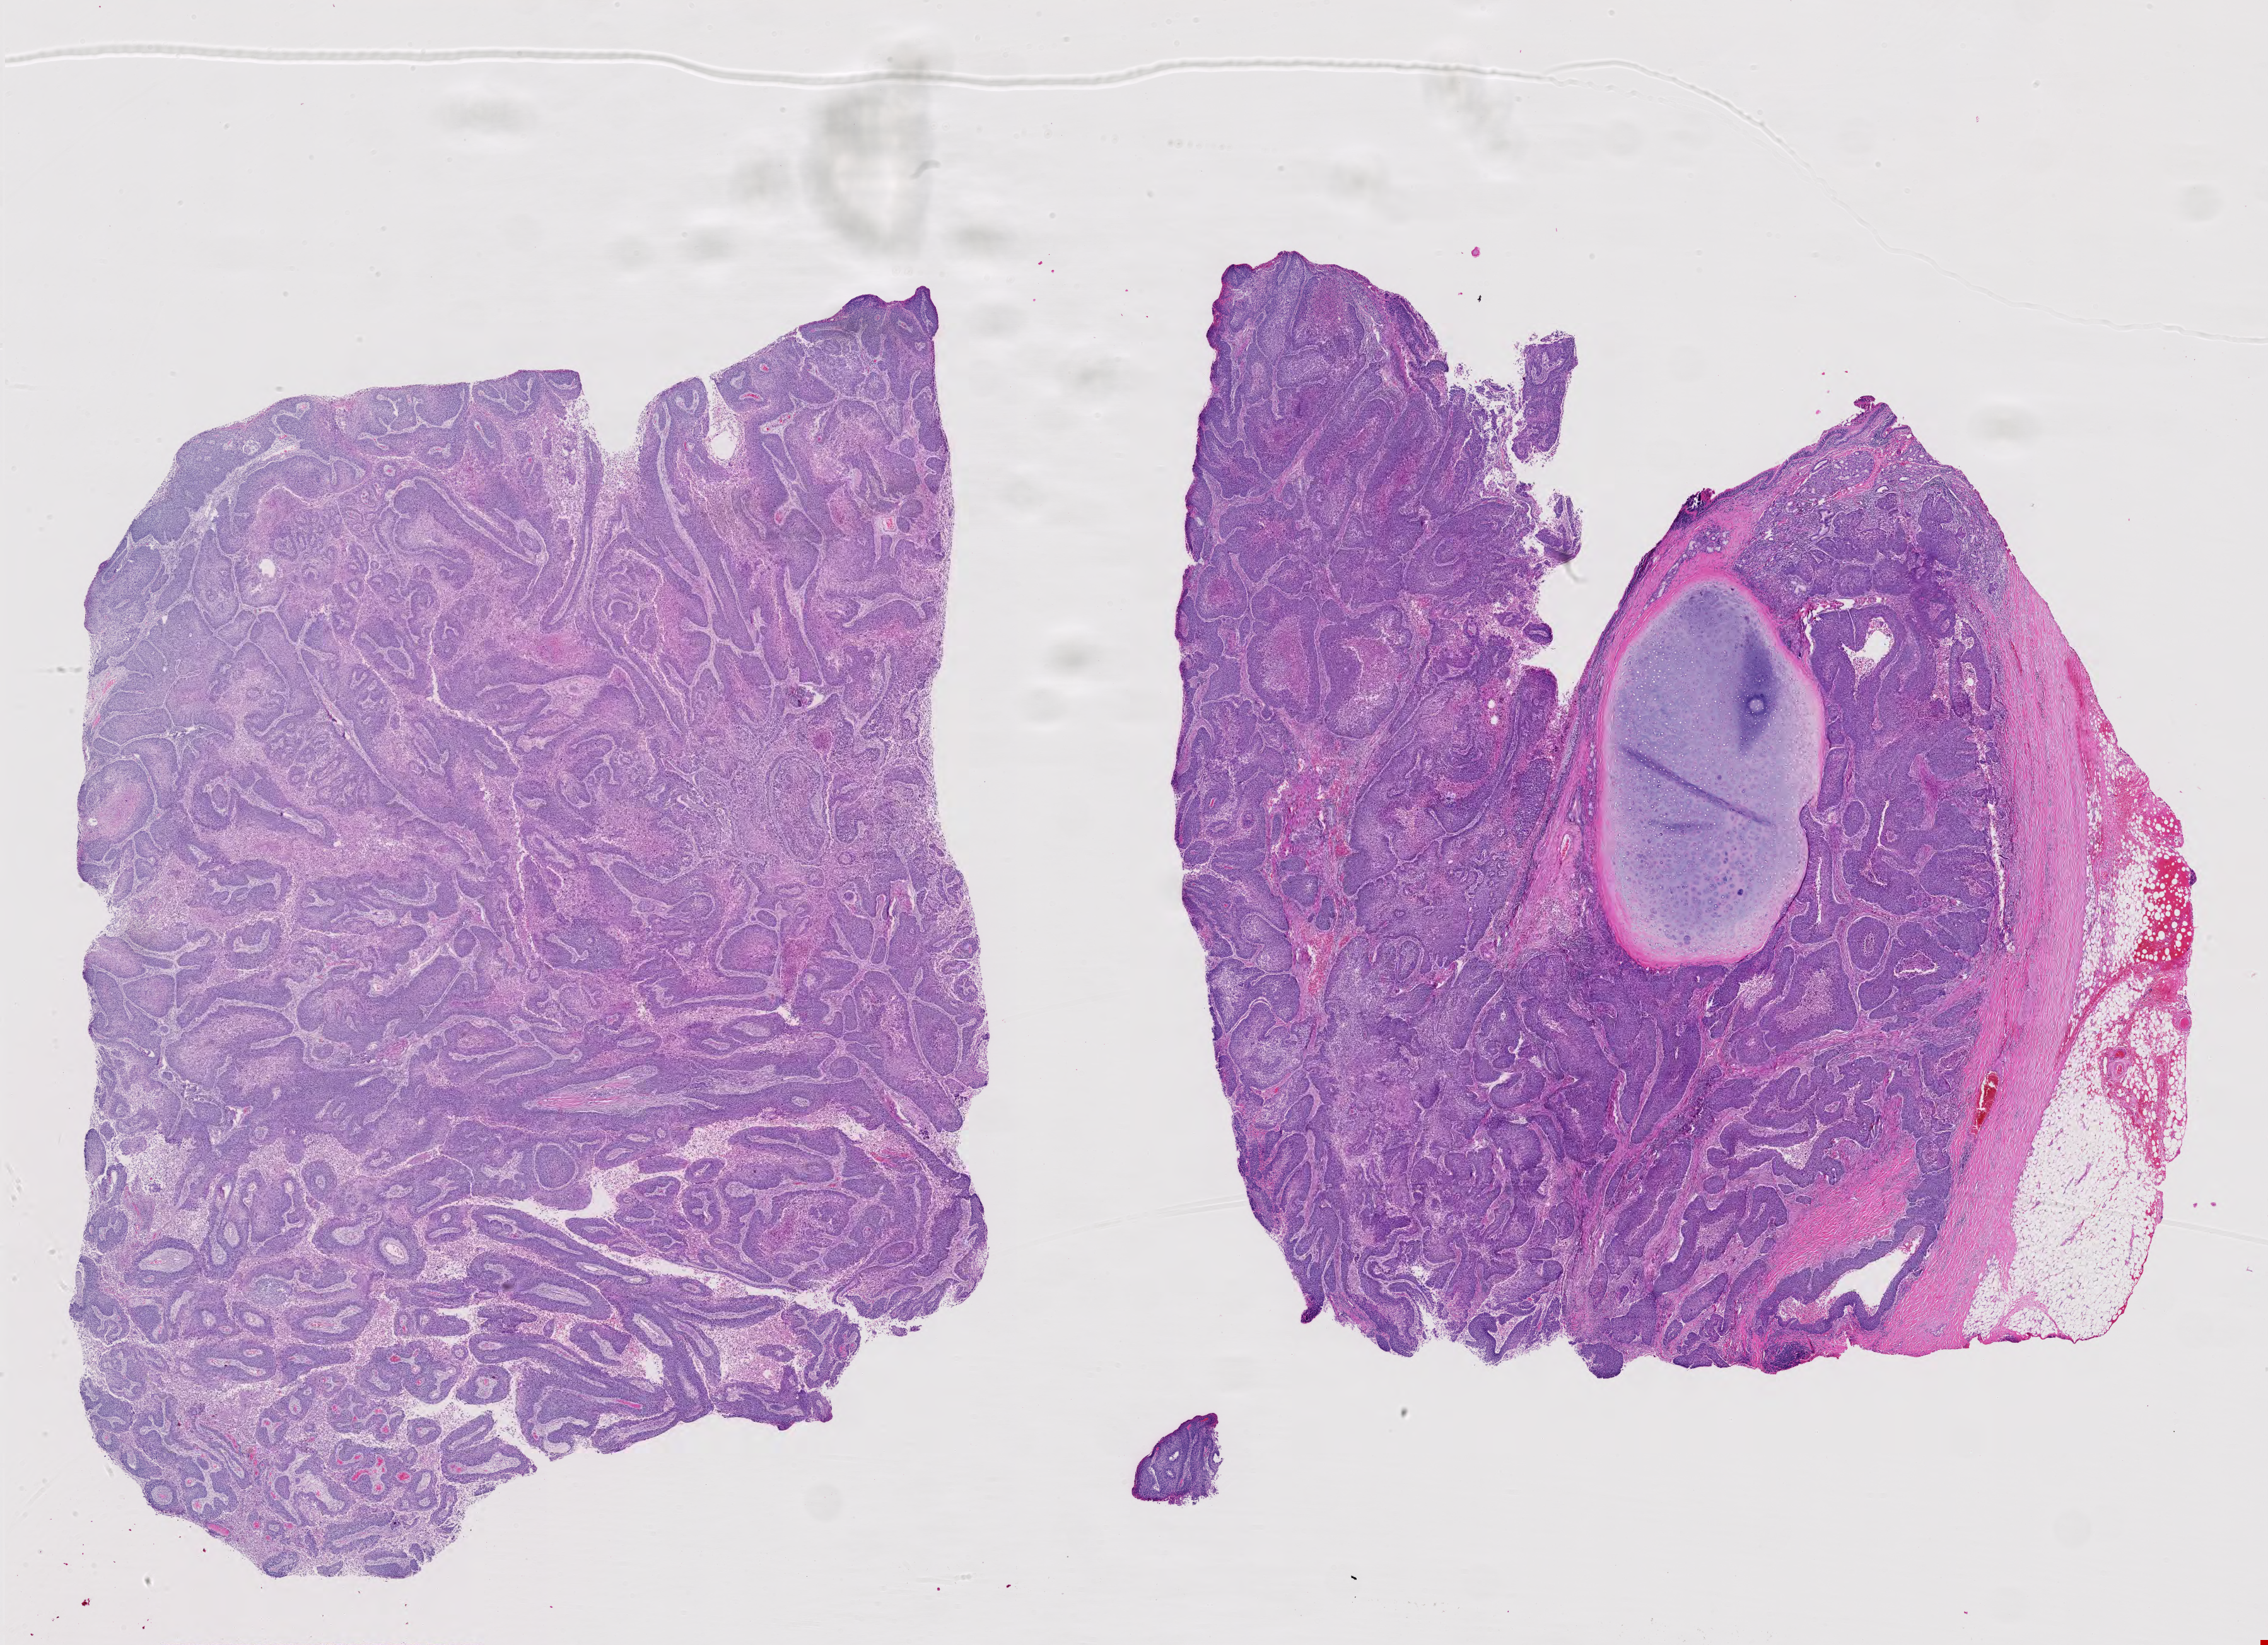
Digitized Hematoxylin and eosin (H&E) stained tissue section (whole slide) — shown as a low-resolution overview of the whole scanned area (about 26.1 x 18.9 mm, from a 40x scan), formalin-fixed paraffin-embedded (FFPE) diagnostic section, lung, primary tumour sample. Patient: male, age at initial diagnosis 70 years.
Pathologic diagnosis: Squamous cell carcinoma, NOS. AJCC pathologic stage: IIB (7th edition). TNM: T3 N0 M0.